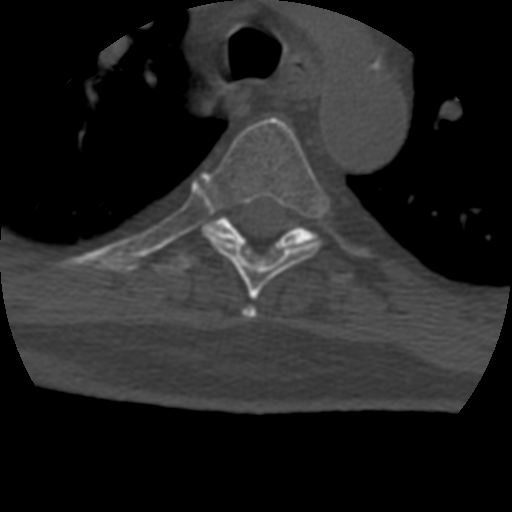
CT including the spine, one axial slice; slice 314 of 399 in the series (ordered by position); bone window (W 1800 / L 400 HU); 512 × 512 image matrix. Patient age 69 years. From the clinical record (not read from this slice): primary cancer: prostate.
Outlined on this slice (semi-automatic segmentation, software-assisted and operator-edited):
- T4 vertebra: bounding box [x1, y1, x2, y2] px = [242, 306, 257, 318]
- T5 vertebra: [202, 118, 329, 300]
- T6 vertebra: [154, 216, 316, 273]